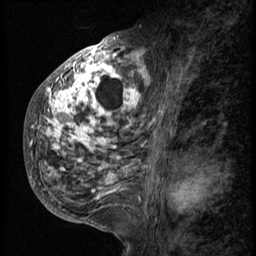
Breast MRI (dynamic contrast-enhanced), one sagittal slice; slice 30 of 58 in the series (ordered by position); 3 images stored at this slice position (order not interpretable as contrast timing); 1.5 T; TE 4.2 ms, TR 9 ms; 256 × 256 image matrix. Patient: female, 50 years. From the clinical record (not read from this slice): setting: breast cancer imaged before/during neoadjuvant chemotherapy; receptor status: triple-negative.
Annotated regions visible in this slice (semi-automatically segmented with operator editing):
- analysis volume of interest (the breast-tissue region the enhancement analysis was run in; not a lesion): bounding box [x1, y1, x2, y2] px = [25, 48, 150, 214]
- tumour enhancement mask (voxels above the 140 % enhancement threshold inside the analysis volume of interest): [30, 48, 149, 200]